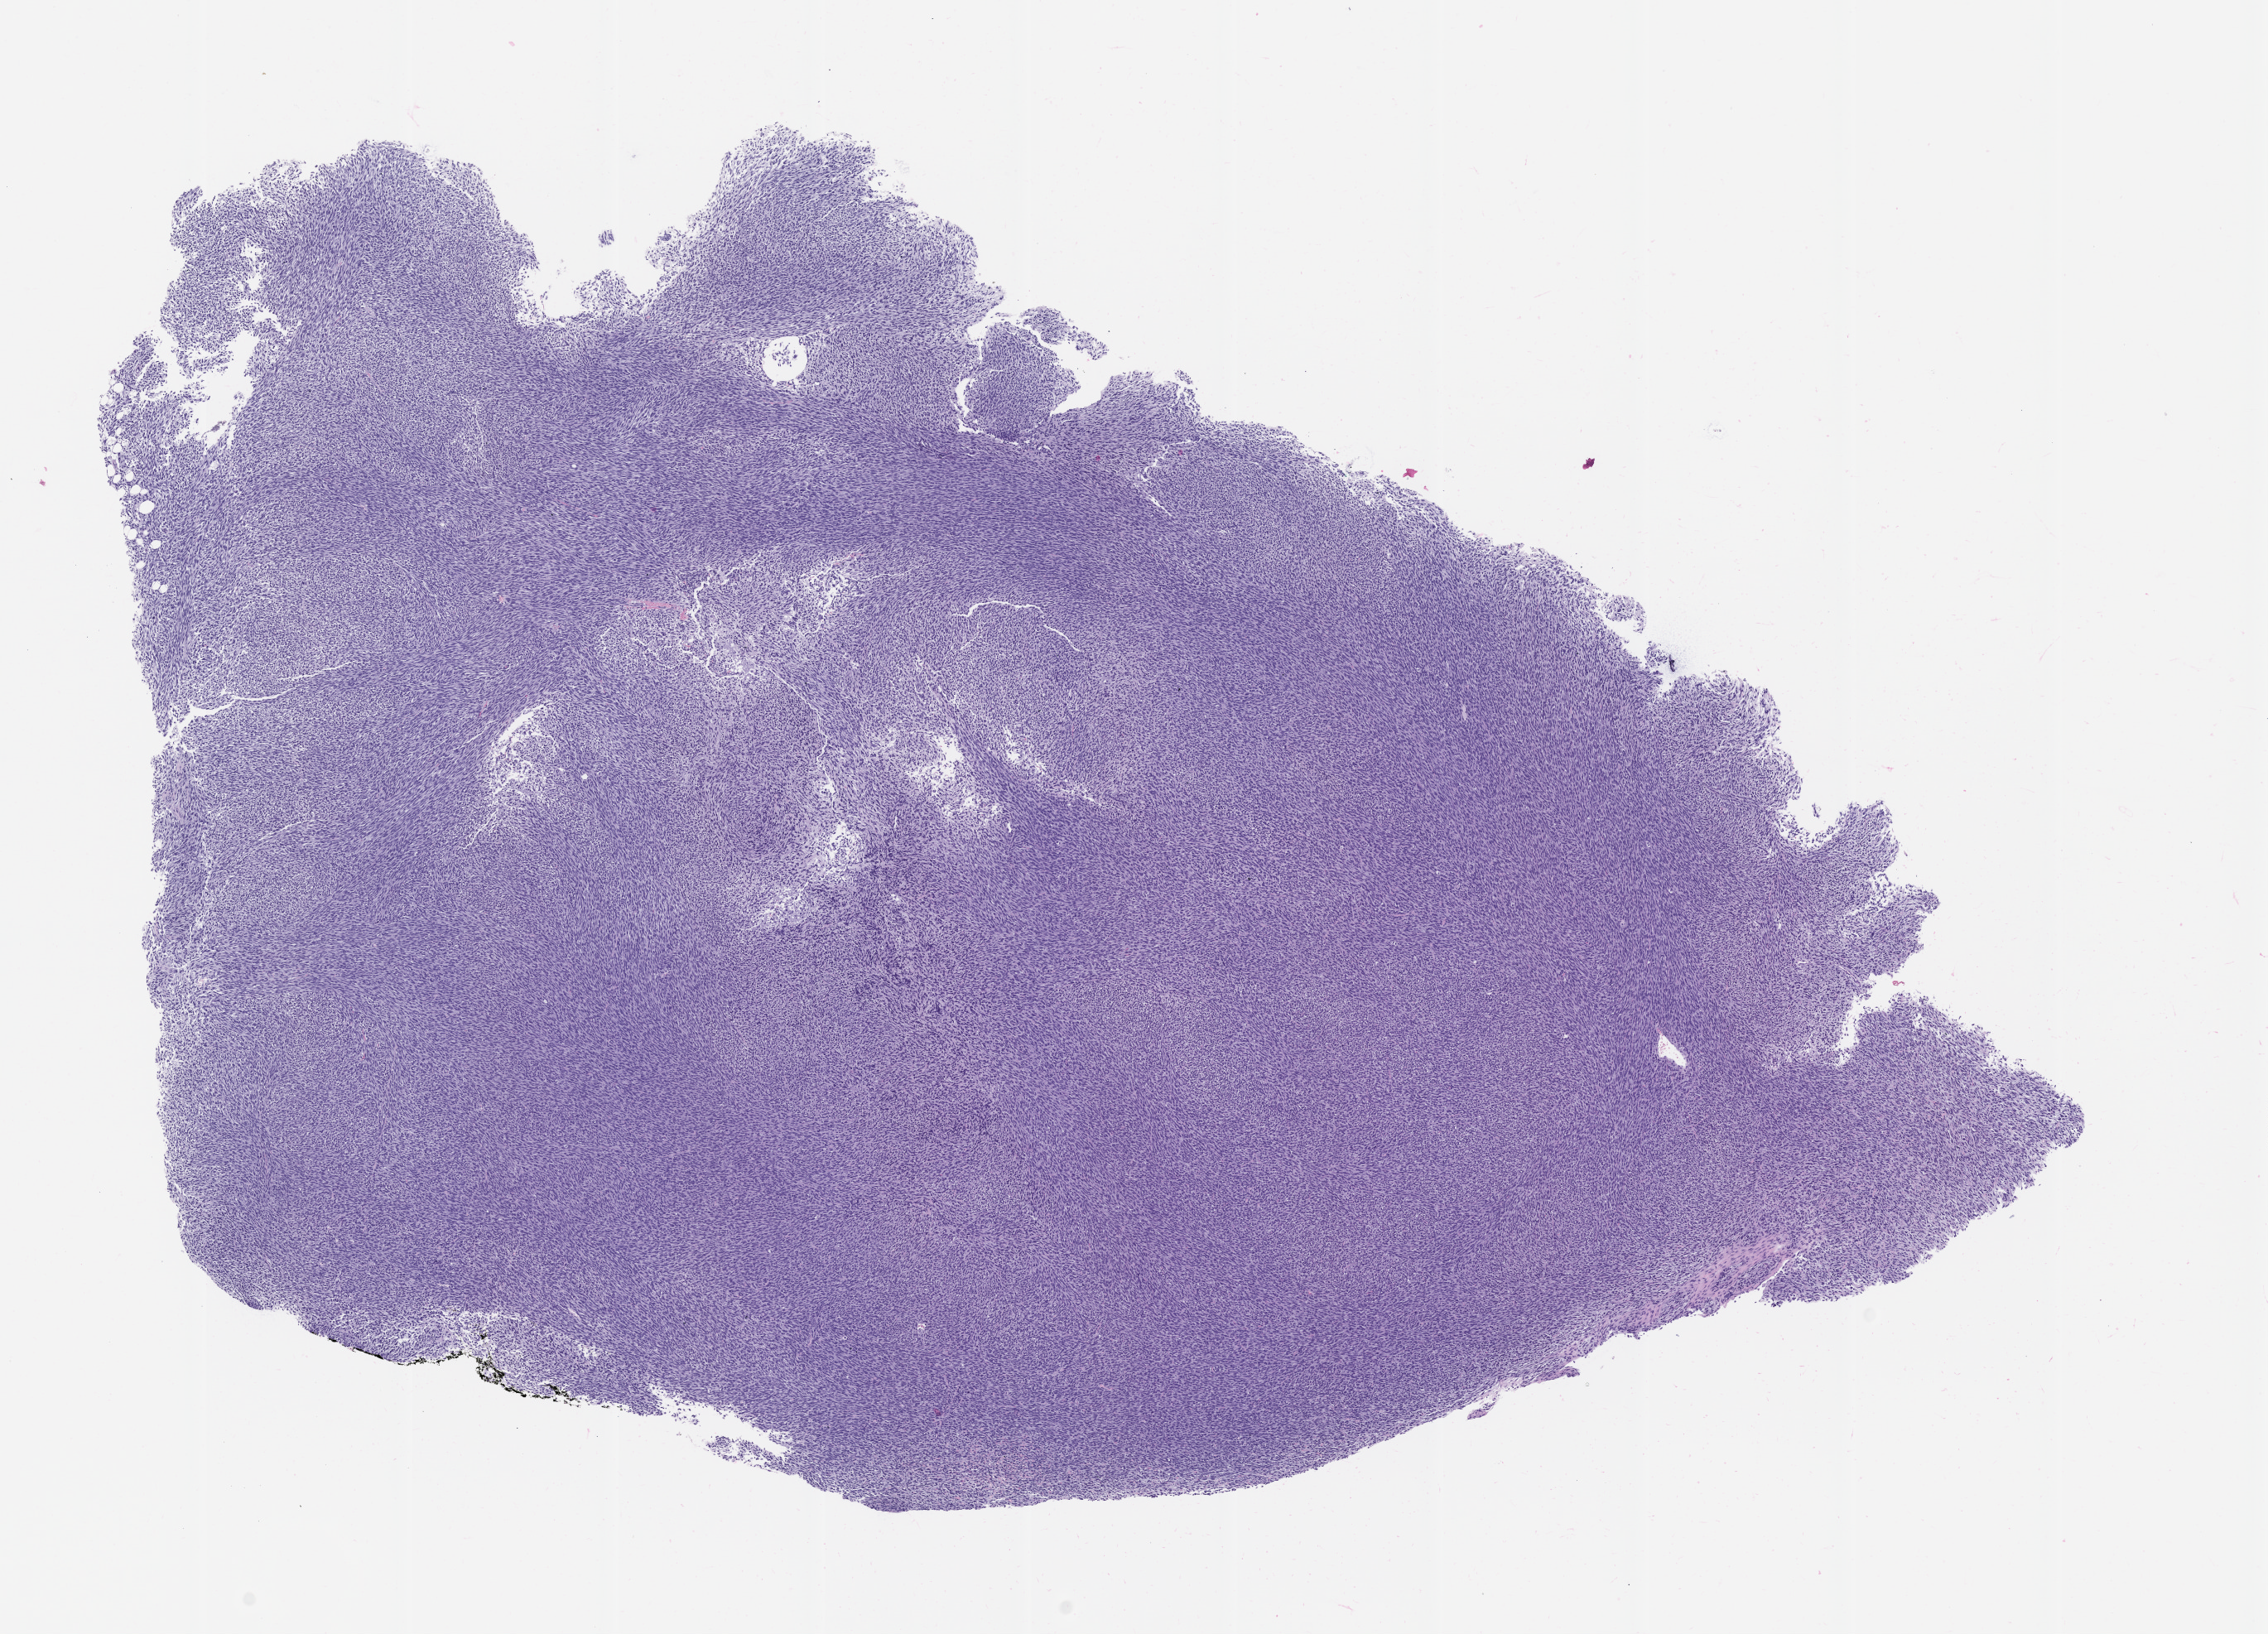
Haematoxylin and eosin whole-slide image of a patient-derived xenograft (PDX) tumor grown in a mouse, passage 1, shown as a low-resolution overview of the whole scanned area (about 11.0 x 7.9 mm); formalin-fixed paraffin-embedded section; originating tumor site category: musculoskeletal.
Originating patient diagnosis: Synovial Sarcoma.